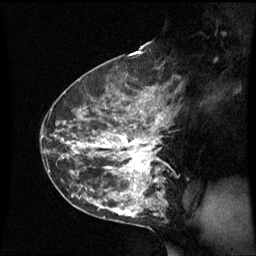
Breast MRI (dynamic contrast-enhanced), one sagittal slice. Slice 34 of 60 in the series (ordered by position). Dynamic contrast-enhanced series, image 2 of 3 at this slice position (ordered by acquisition). 1.5 T. TE 4.2 ms, TR 8.9 ms. 2.4 mm slice thickness. 256 × 256 image matrix. Patient: female, 42 years. From the clinical record (not read from this slice): setting: breast cancer imaged before/during neoadjuvant chemotherapy; receptor status: HER2-positive.
Annotated regions visible in this slice (semi-automatic segmentation, software-assisted and operator-edited):
- analysis volume of interest (the breast-tissue region the enhancement analysis was run in; not a lesion): bounding box <62,93,168,210> (left, top, right, bottom; pixels)
- tumour enhancement mask (voxels above the 70 % enhancement threshold inside the analysis volume of interest): <69,95,164,199>